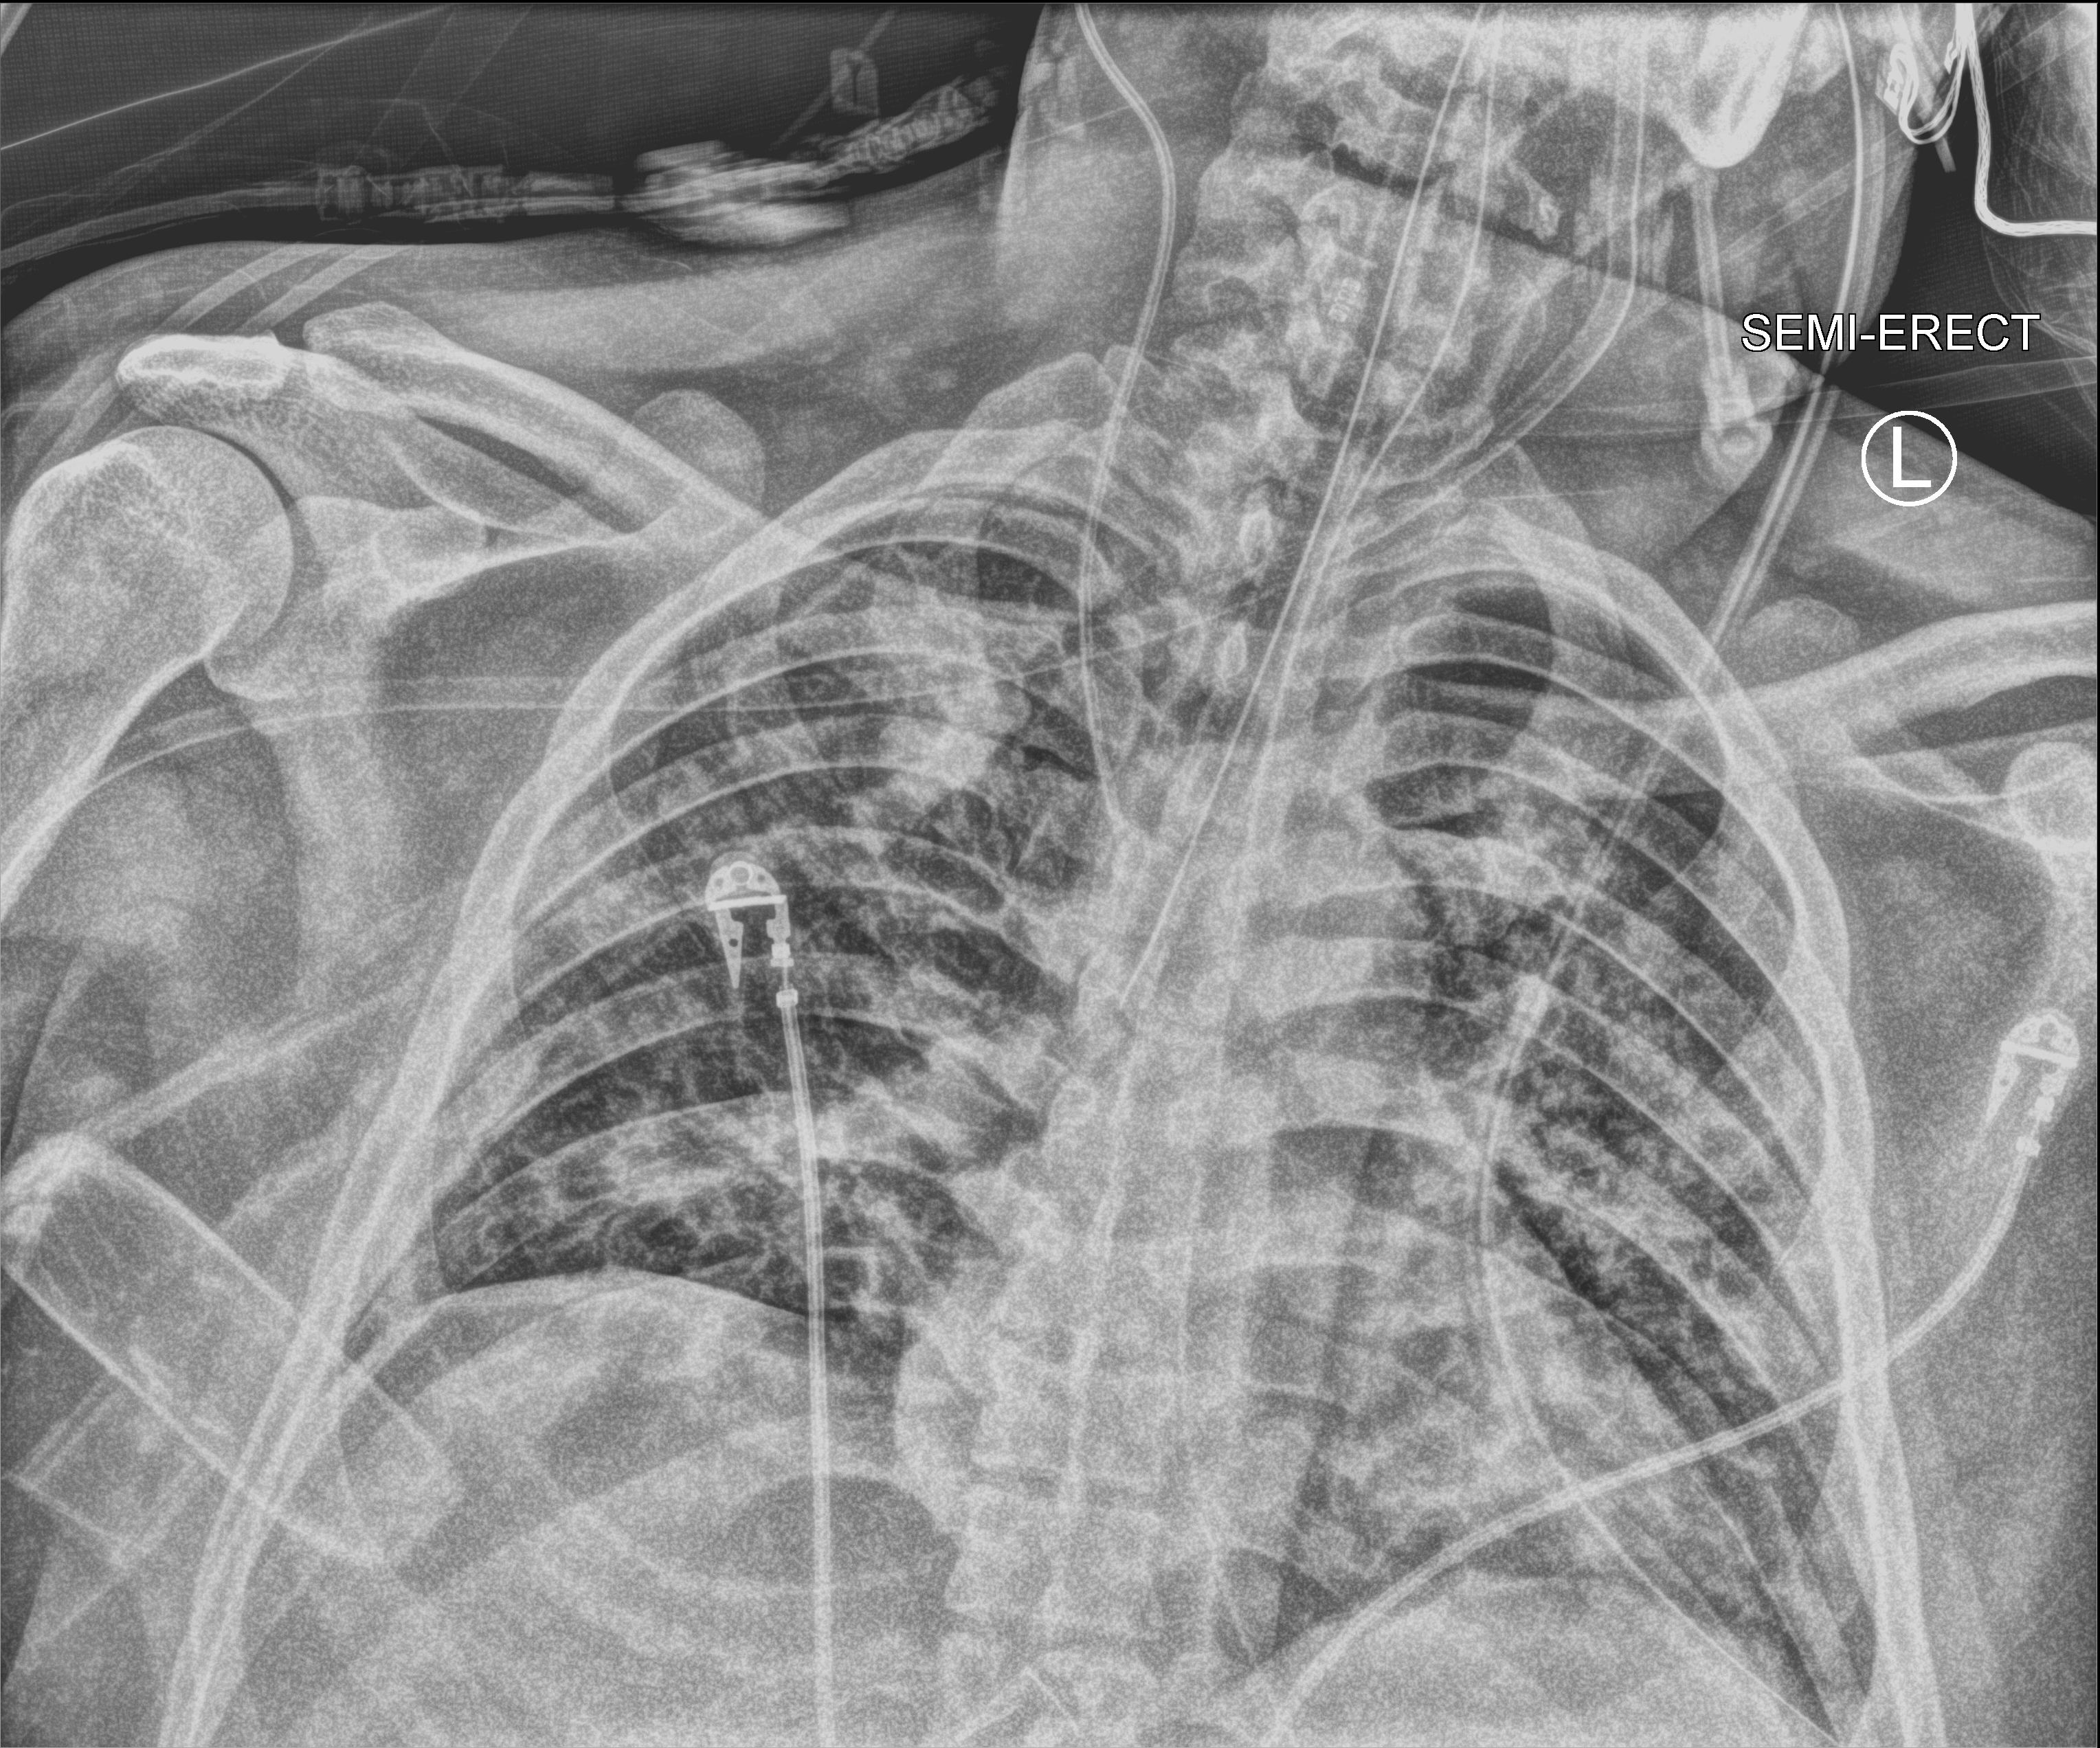
Chest X-ray (portable), anteroposterior (AP) projection. Patient hospitalised with COVID-19; male, aged 18–59 years.
Hospital-stay facts (about this admission, not read from this image; timing relative to this image not recorded): mechanically ventilated during this hospital stay: yes; length of hospital stay: 29 days.